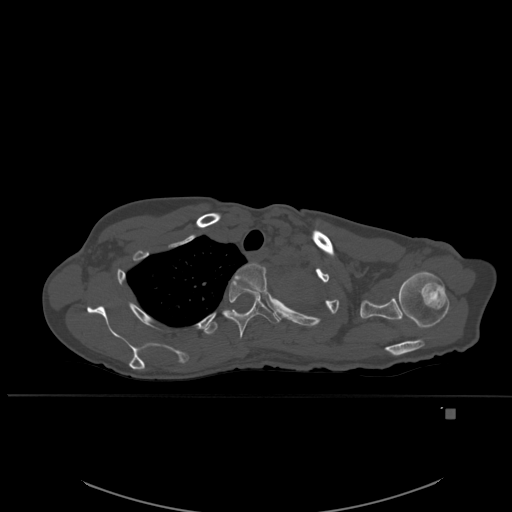
CT including the spine, one axial slice. Position 426 of 537 along the scan axis. Bone window (W 1800 / L 400 HU). 1.5 mm slice thickness. 512 × 512 image matrix. Patient: female, 45 years. Case-level facts recorded for this patient, not image findings: primary cancer: lung.
Annotated regions visible in this slice (semi-automatic segmentation, software-assisted and operator-edited):
- T2 vertebra: bounding box <233,263,267,294> (left, top, right, bottom; pixels)
- T3 vertebra: <224,279,280,340>
- T4 vertebra: <202,311,225,335>